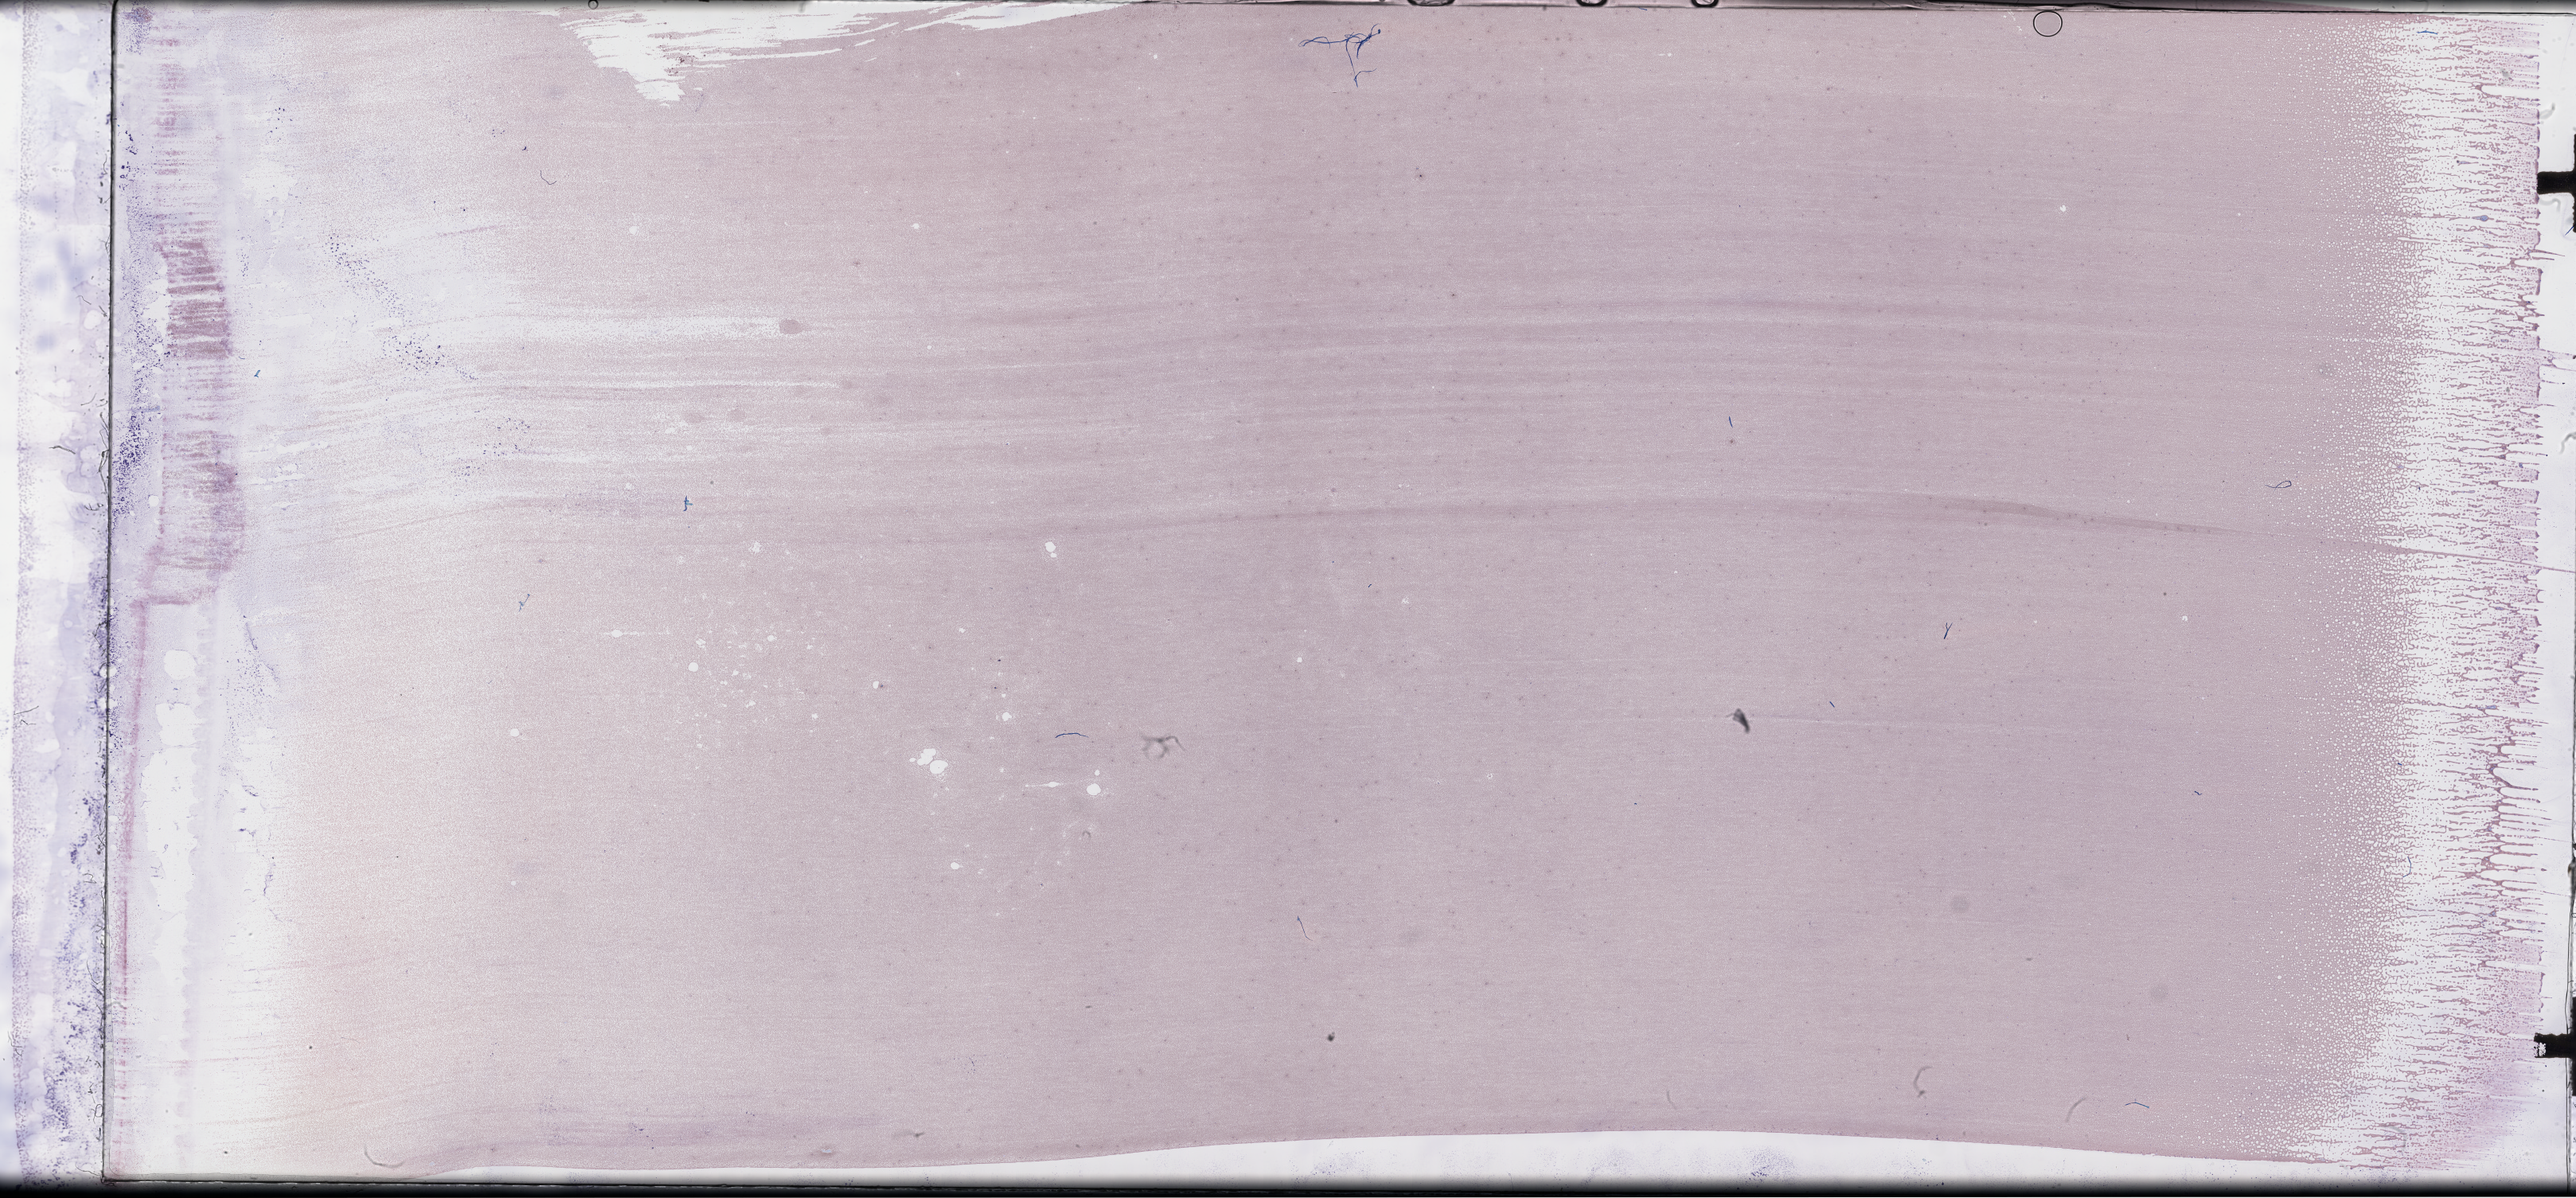
Whole-slide image of a whole blood smear, Wright-Giemsa stain, whole scanned area (about 52.3 x 24.3 mm) shown as a low-resolution overview; collected on treatment. Male patient.
Patient diagnosis: Plasma Cell Myeloma.